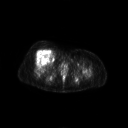
FDG PET of an extremity soft-tissue mass (from a PET/CT study), one axial slice. 3.27 mm slice thickness. 128 × 128 image matrix, field of view 700 × 700 mm. Female patient, age 56 years. Case-level facts recorded for this patient, not image findings: histological type: malignant solitary fibrous tumor; grade: intermediate; site of the primary tumour: right thigh.
Annotated regions visible in this slice (expert contour drawn on MRI and transferred to this co-registered scan by the dataset authors):
- gross tumour volume including surrounding oedema: box from (x=35, y=49) to (x=52, y=62) px
- gross tumour volume (mass): (x=35, y=50)–(x=51, y=62)